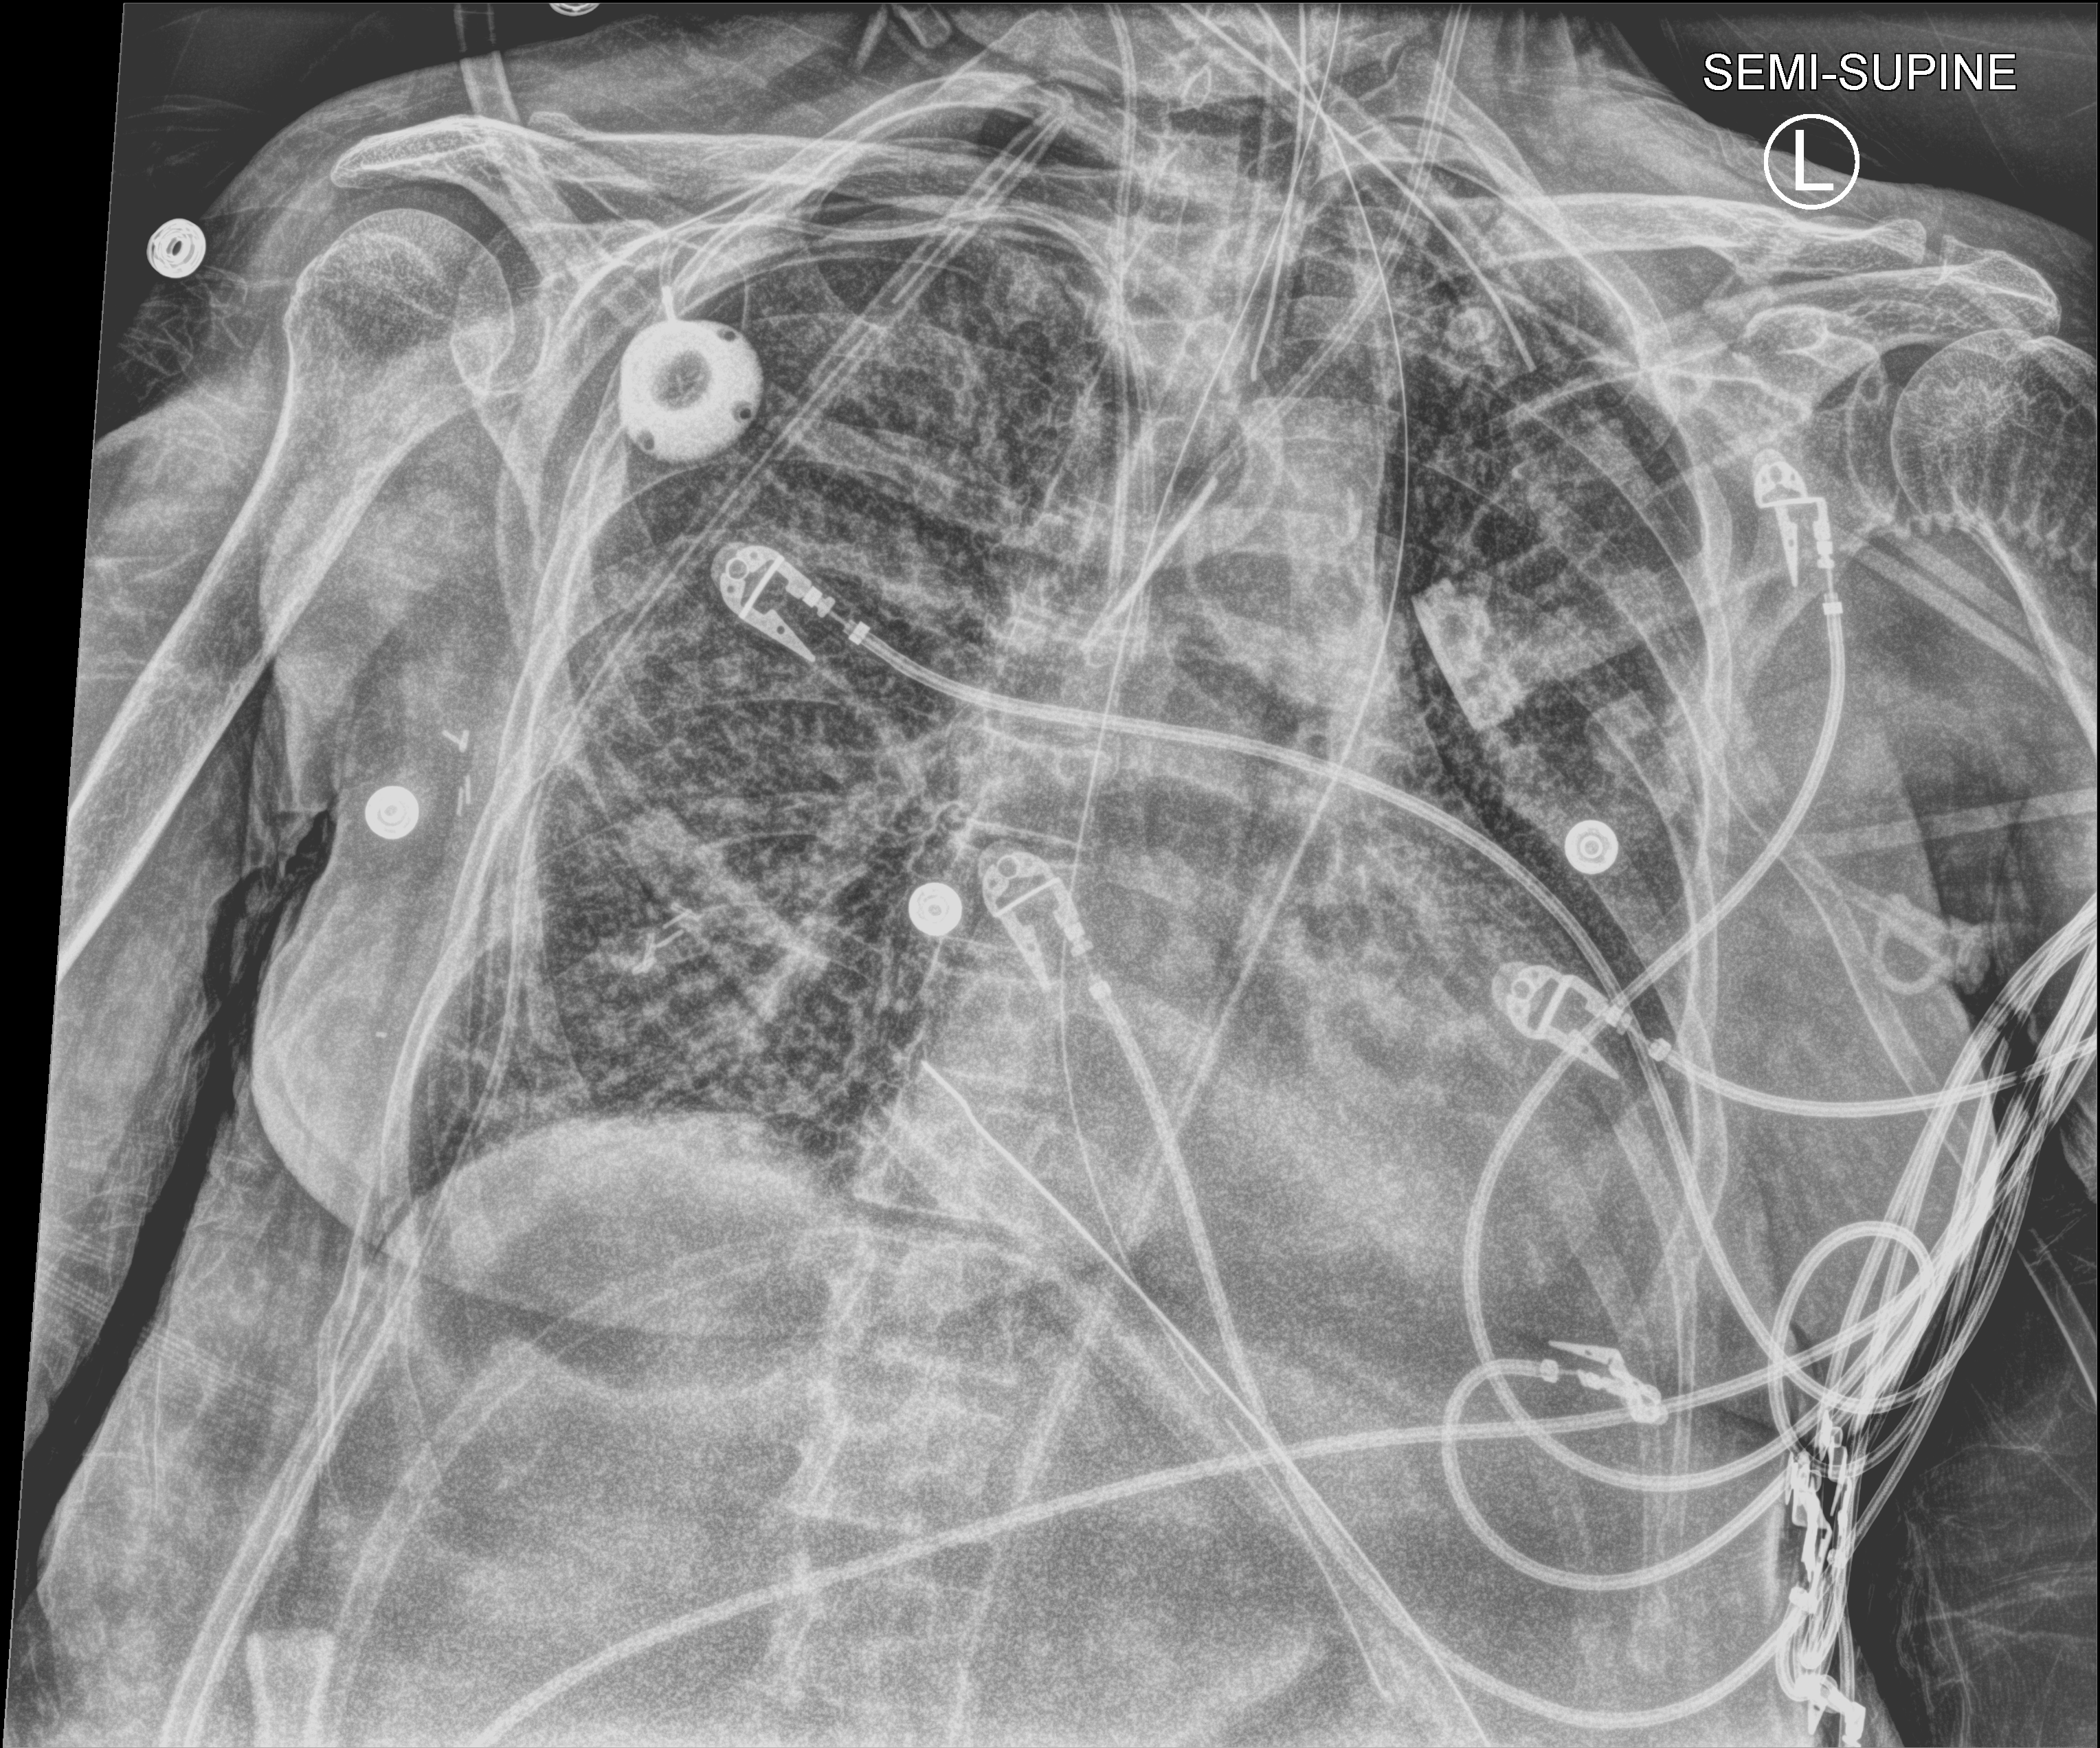
Chest X-ray (portable), anteroposterior (AP) projection. Female patient hospitalised with COVID-19, age 60–74 years.
Admission-level facts for this patient (not findings on this image; timing relative to this image not recorded):
- mechanically ventilated during this hospital stay: yes
- other chronic lung disease (admission record): no